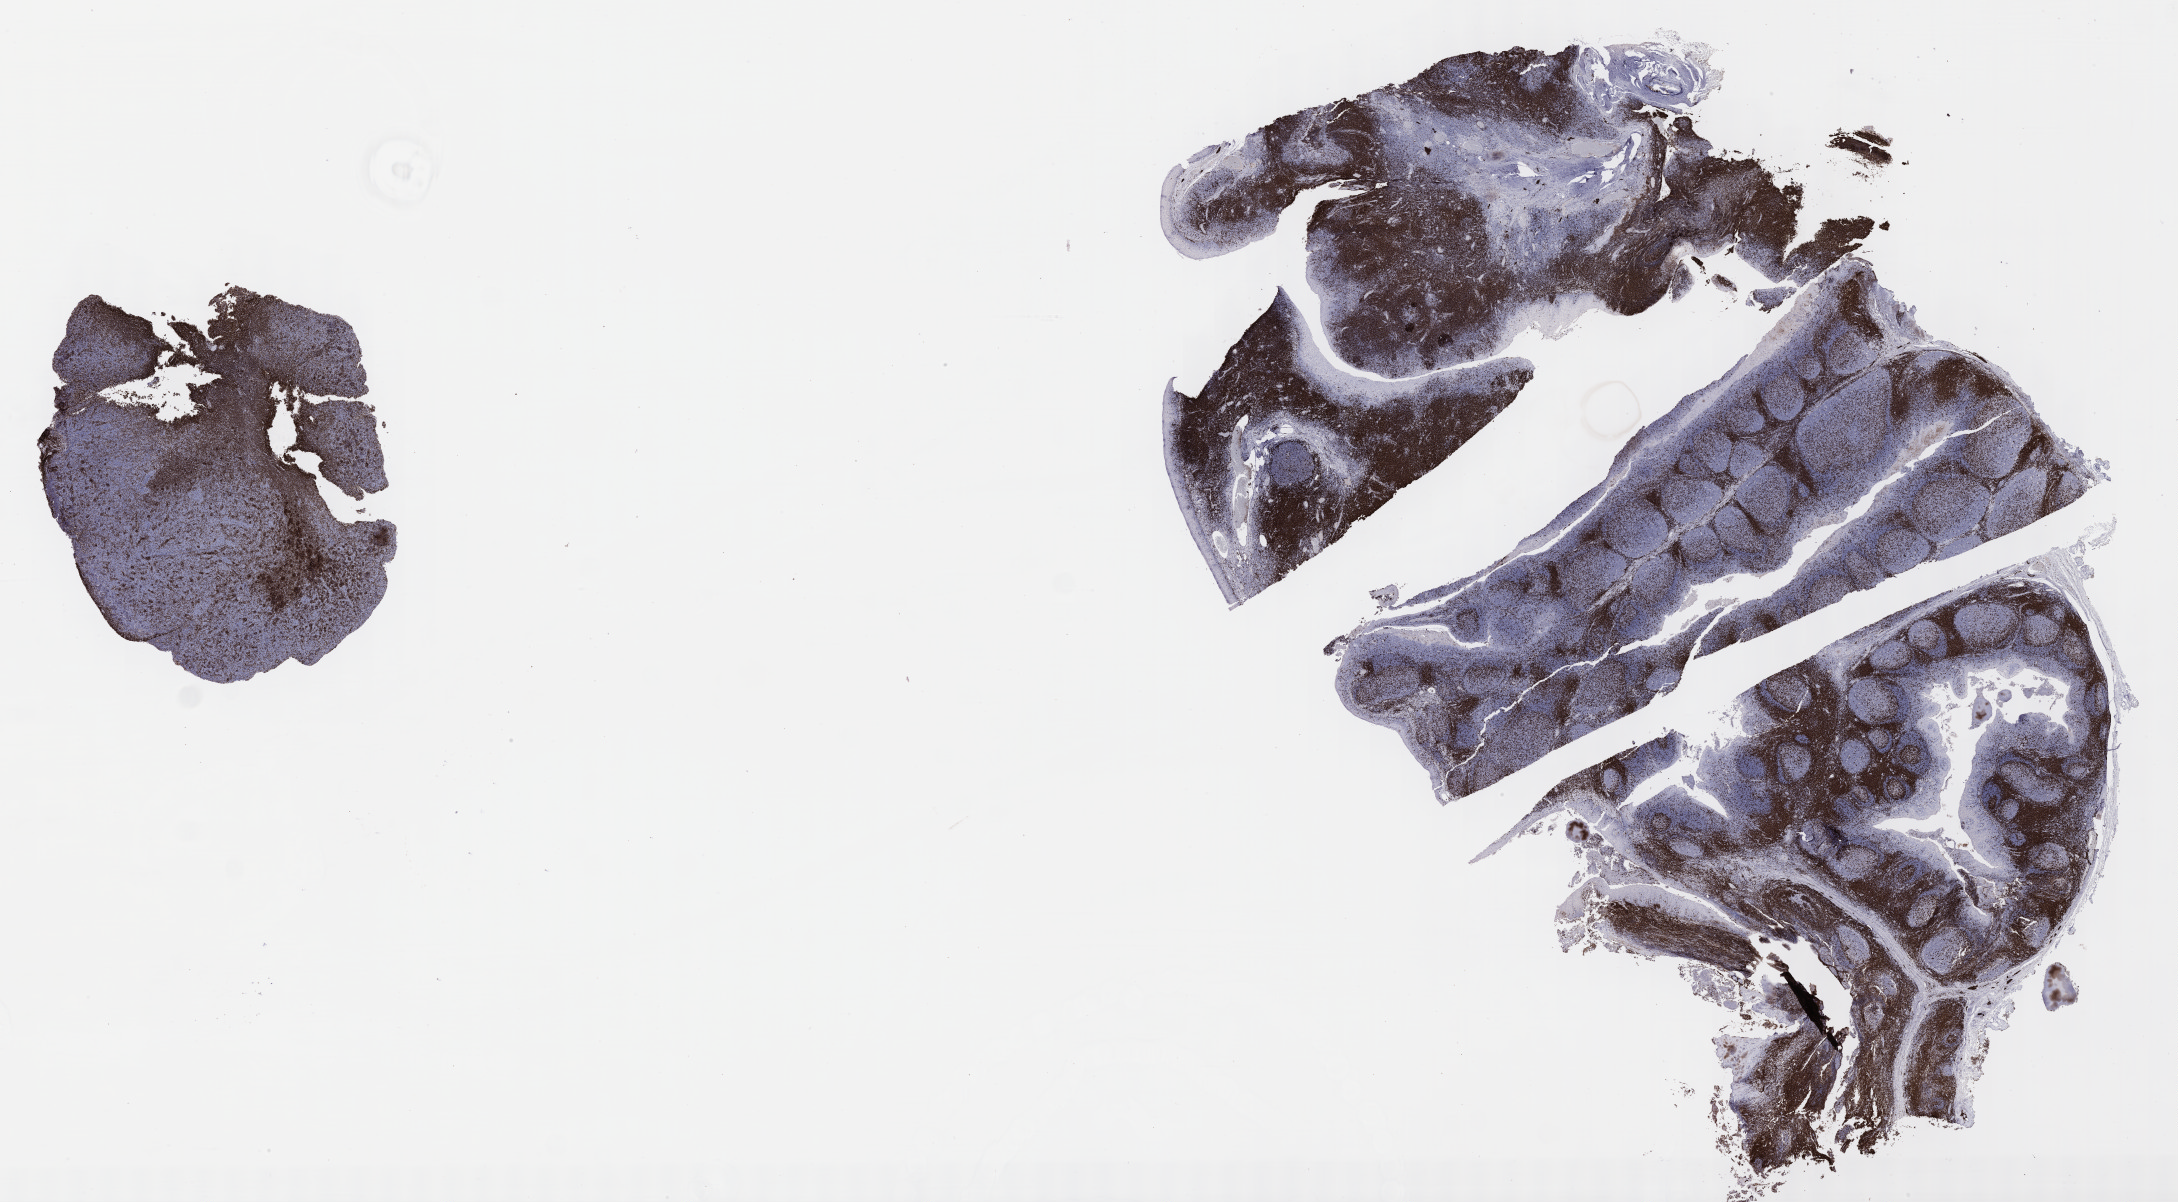
IHC for CD3, whole-slide image — shown as a low-resolution overview of the whole scanned area (about 35.2 x 19.4 mm); specimen: tumor tissue; site: liver. Patient: male, age 46 years.
Diagnosis: Diffuse large B-cell lymphoma, NOS.